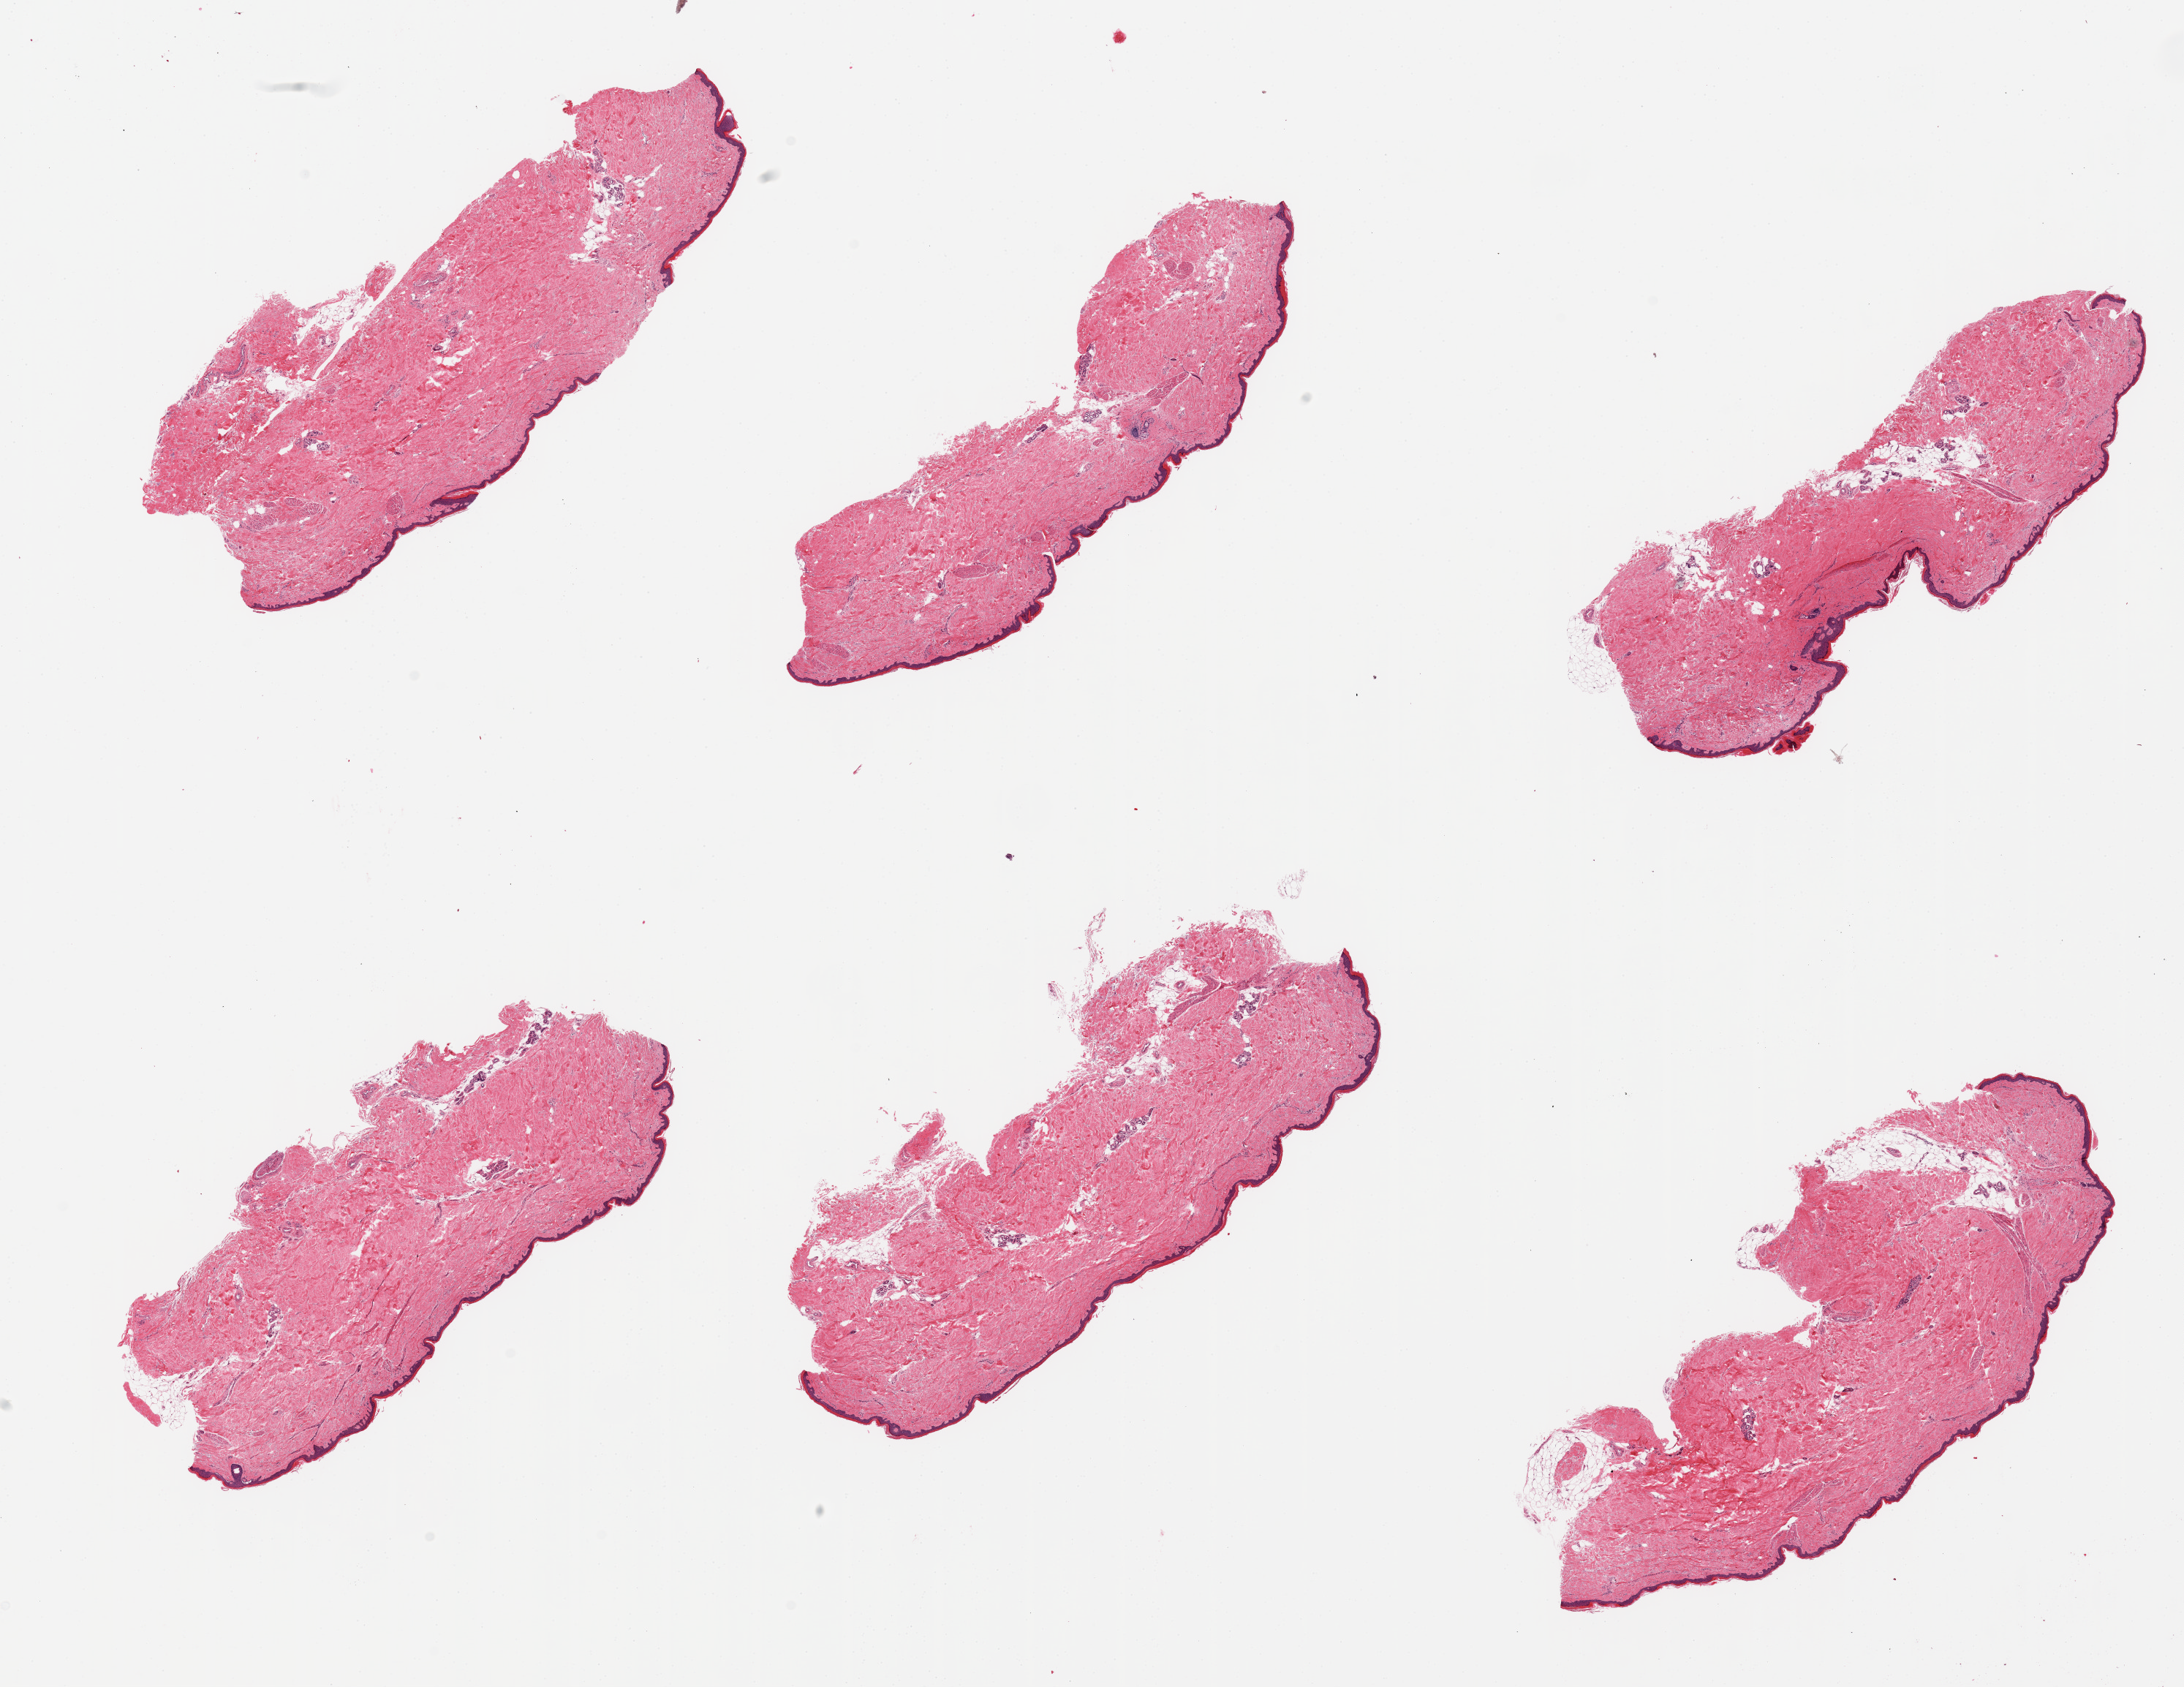
Digitized H&E-stained section, low-resolution overview of the scanned area, about 23.6 x 18.2 mm (slide scanned at 20x), PAXgene-fixed paraffin-embedded (PFPE) section, target tissue: skin of lower leg, donor tissue sample.
Reviewer comment on this tissue sample: 6 pieces; ~10% external/internal fat; epidermis measures up to 40um.